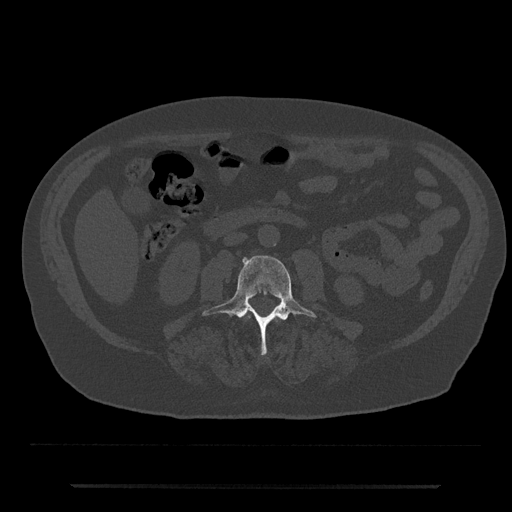
CT including the spine, one axial slice. Slice 414 of 797 in the series (ordered by position). Reconstruction kernel Br40s/3. 120 kVp. Bone window (W 1800 / L 400 HU). 0.5 mm slice thickness. 512 × 512 image matrix, field of view 434 × 434 mm. Male patient, age 80 years. From the clinical record (not read from this slice): primary cancer: prostate.
Annotated regions visible in this slice (semi-automatic segmentation, software-assisted and operator-edited):
- L2 vertebra: box from (x=247, y=316) to (x=249, y=318) px
- L3 vertebra: (x=202, y=255)–(x=317, y=356)